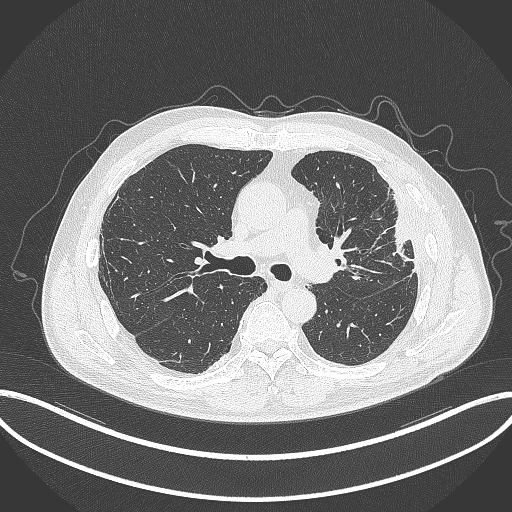
Chest CT, one axial slice; slice 209 of 382 in the series (ordered by position); reconstruction kernel B70f; 120 kVp; lung window (W 1500 / L -600 HU); 1 mm slice thickness; 512 × 512 image matrix, field of view 415 × 415 mm. Male patient, age 64 years. Case-level facts recorded for this patient, not image findings: clinical TNM (as recorded): T4 N1 M0; histopathological grade: G3.
Annotated regions visible in this slice (bounding box drawn by a radiologist):
- lung tumour (recorded histology: adenocarcinoma): bounding box <381,192,419,265> (left, top, right, bottom; pixels)